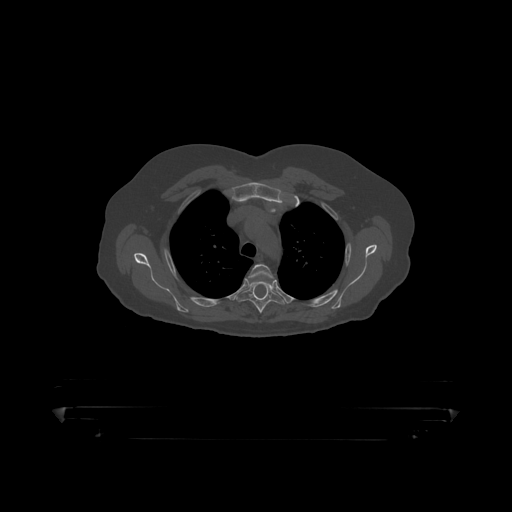
CT including the spine, one axial slice. Position 344 of 390 along the scan axis. Reconstruction kernel STANDARD. Bone window (W 1800 / L 400 HU). 512 × 512 image matrix, field of view 650 × 650 mm. Male patient, age 60 years. From the clinical record (not read from this slice): primary cancer: prostate.
Outlined on this slice (semi-automatically segmented with operator editing):
- T3 vertebra: box from (x=248, y=264) to (x=273, y=286) px
- T4 vertebra: (x=237, y=282)–(x=285, y=314)